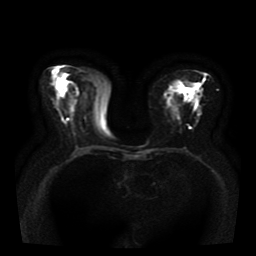
Breast MRI, one axial slice; slice 18 of 41 in the series (ordered by position); diffusion-weighted series; image 2 of 4 stored at this slice position (different b-values; order by instance number); 1.5 T; 256 × 256 image matrix, field of view 330 × 330 mm. Female patient.
Outlined on this slice (manually delineated by an expert):
- tumour on diffusion-weighted imaging: bounding box (x1, y1, x2, y2) in pixels: (191, 89, 196, 96)